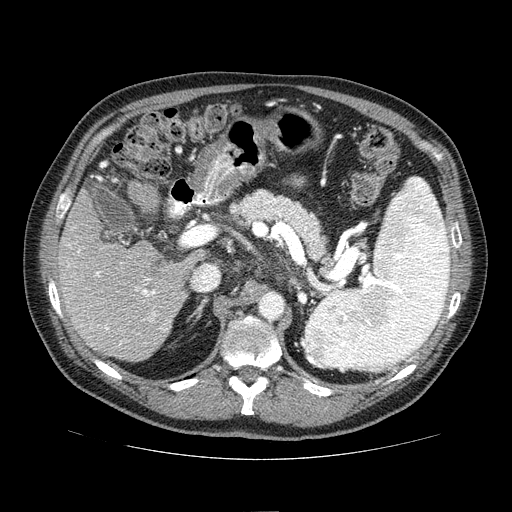
Contrast-enhanced abdominal CT (liver protocol), one axial slice; slice 38 of 81 in the series (ordered by position); reconstruction kernel STANDARD; 100 kVp; one of 2 acquisitions stored at this slice position; soft-tissue window (W 400 / L 40 HU); 2.5 mm slice thickness; 512 × 512 image matrix, field of view 400 × 400 mm. Case-level facts recorded for this patient, not image findings: diagnosis: hepatocellular carcinoma (patient treated with transarterial chemoembolisation; whether this scan precedes or follows treatment is not stated here); TNM stage (as recorded): Stage-IIIA; Child-Pugh class: A; tumour differentiation: well differentiated; tumour nodularity: multinodular.
Annotated regions visible in this slice (semi-automatic segmentation, software-assisted and operator-edited):
- liver parenchyma outside the tumour (the mass and vessels are separate outlines, so this box may not span the whole liver): bounding box [x1, y1, x2, y2] px = [58, 178, 192, 360]
- liver vessels: [67, 179, 170, 344]